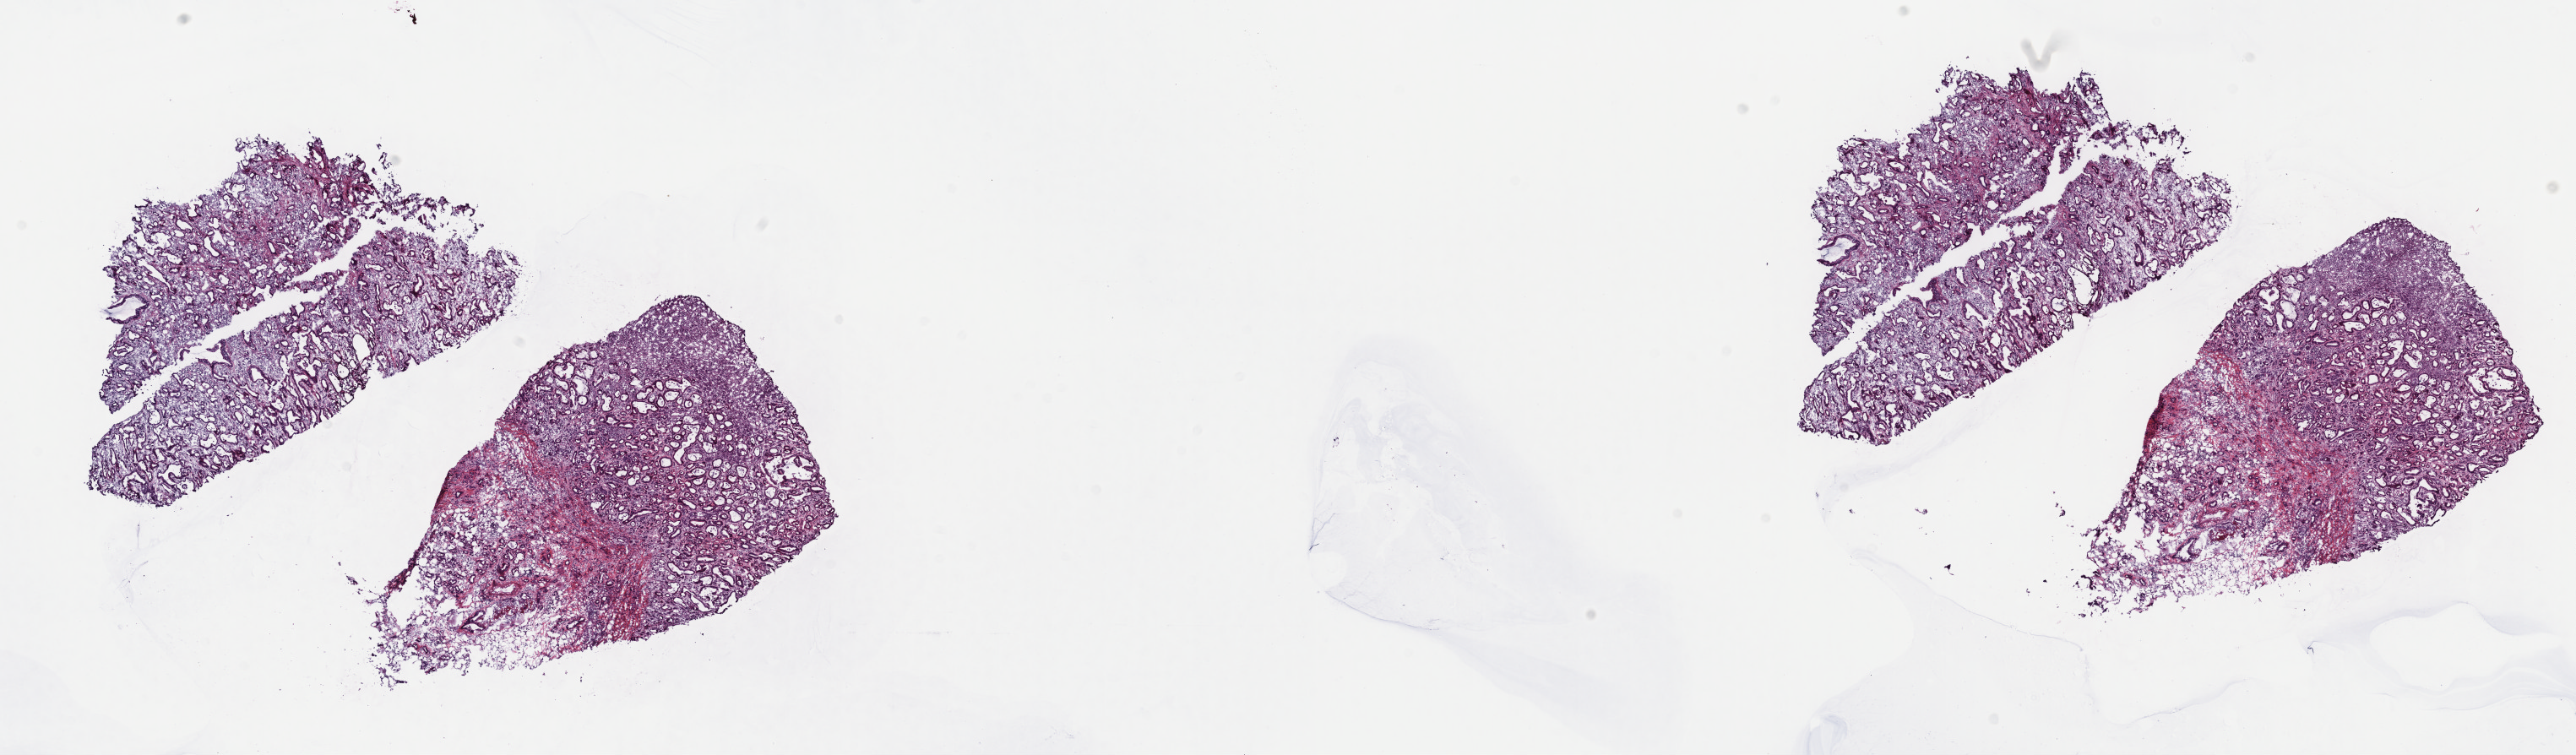
H&E whole-slide image, shown as a low-resolution overview of the whole scanned area (about 24.7 x 7.2 mm, from a 40x scan), frozen section, metastatic tumour sample, sampled site not recorded. Male patient; age at initial diagnosis 70 years. Slide review estimates, as recorded: tumour cells 100%, tumour nuclei 70%.
This section: metastatic tumour tissue. Patient diagnosis: Adenocarcinoma, NOS.